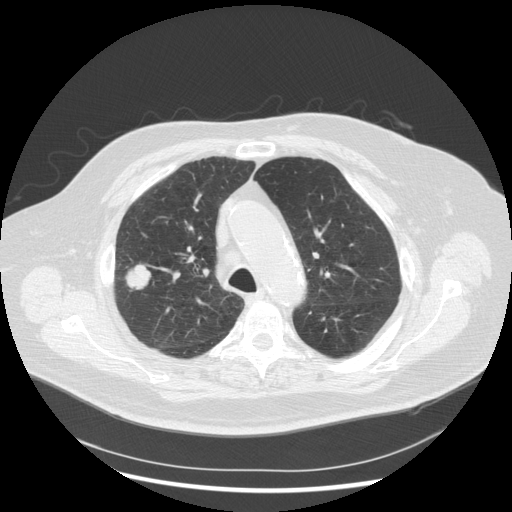
Low-dose screening chest CT, one axial slice. Slice 203 of 263 in the series (ordered by position). Reconstruction kernel STANDARD. Lung window (W 1500 / L -600 HU). 512 × 512 image matrix.
Outlined on this slice (manually delineated by an expert):
- lesion 1 (tumor, upper lobe of right lung): bounding box <126,265,151,290> (left, top, right, bottom; pixels)